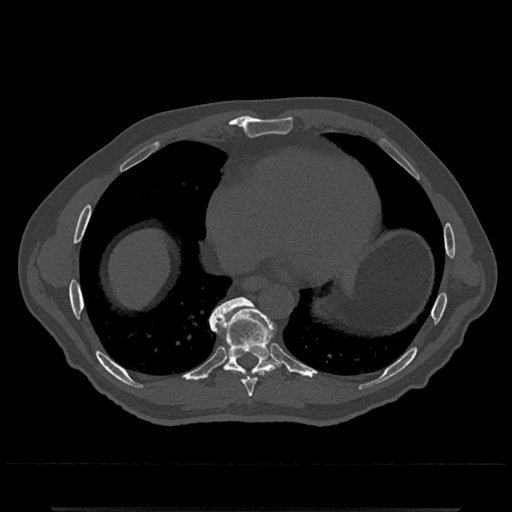
CT including the spine, one axial slice; slice 638 of 797 in the series (ordered by position); 120 kVp; bone window (W 1800 / L 400 HU); 0.5 mm slice thickness; 512 × 512 image matrix, field of view 393 × 393 mm. Male patient, age 67 years. Case-level facts recorded for this patient, not image findings: primary cancer: prostate.
Structures marked on this image (semi-automatically segmented with operator editing):
- T8 vertebra: bounding box [x1, y1, x2, y2] px = [242, 372, 262, 397]
- T9 vertebra: [210, 297, 279, 375]